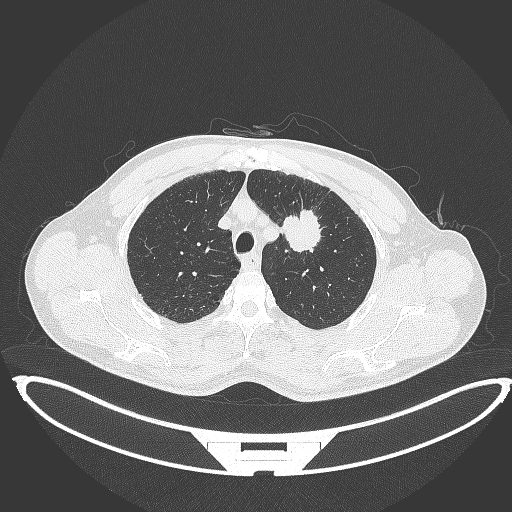
Chest CT, one axial slice. 120 kVp. Lung window (W 1500 / L -600 HU). 1 mm slice thickness. 512 × 512 image matrix. Male patient, age 60 years. From the clinical record (not read from this slice): clinical TNM (as recorded): T2a N0 M0; histopathological grade: G1-G2.
Structures marked on this image (bounding box drawn by a radiologist):
- lung tumour (recorded histology: squamous cell carcinoma): bounding box [x1, y1, x2, y2] px = [279, 209, 325, 252]